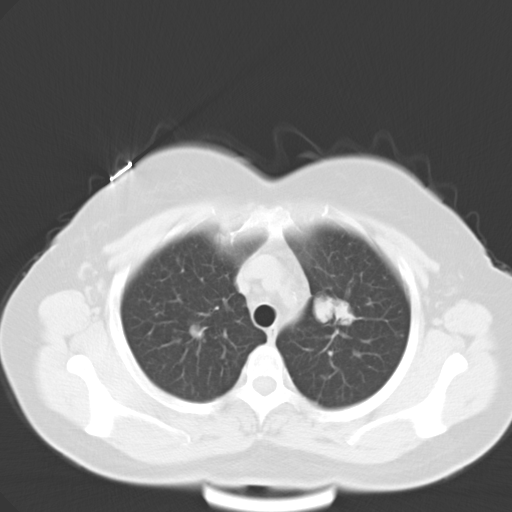
Chest CT, one axial slice; slice 22 of 28 in the series (ordered by position); reconstruction kernel B40f; 120 kVp; lung window (W 1500 / L -600 HU); 10 mm slice thickness; 512 × 512 image matrix, field of view 353 × 353 mm. Female patient, age 53 years. From the clinical record (not read from this slice): clinical TNM (as recorded): T1c N0 M1a.
Structures marked on this image (rectangle marked by the reading radiologist):
- lung tumour (recorded histology: adenocarcinoma): bounding box (x1, y1, x2, y2) in pixels: (309, 289, 355, 327)